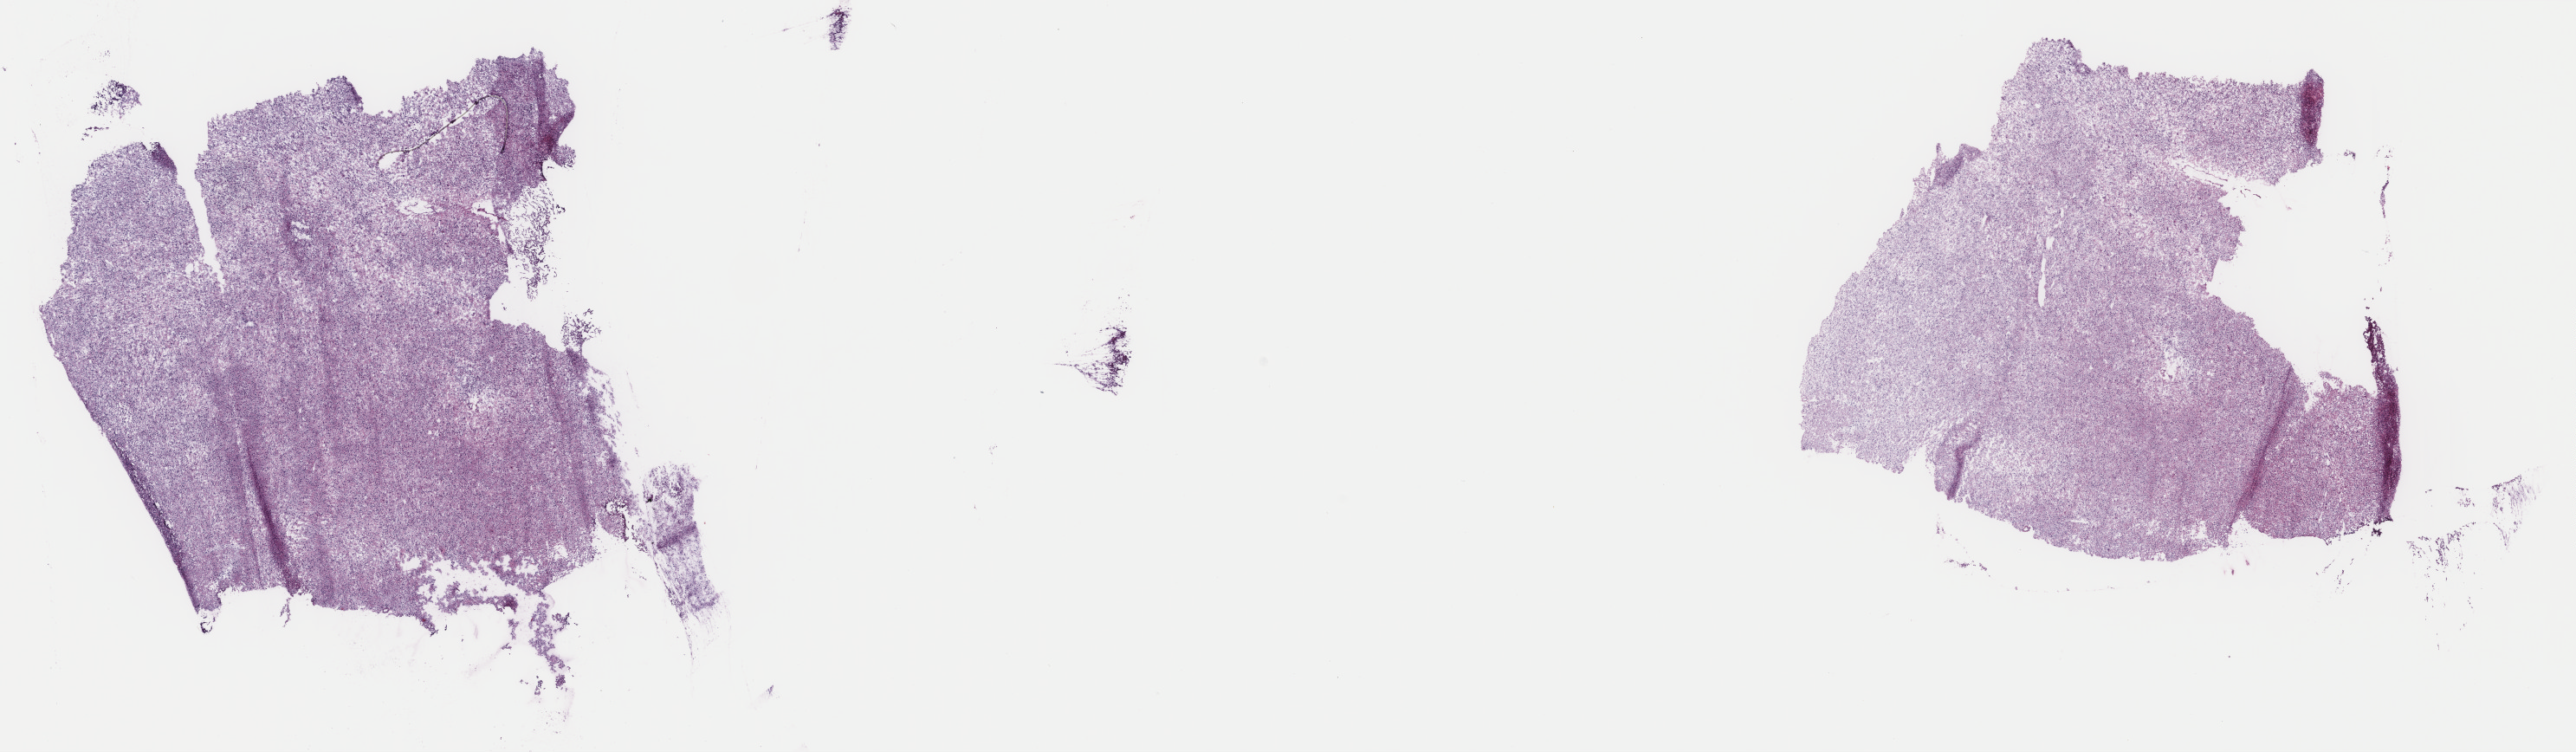
Digitized H&E-stained tissue section (whole slide) — low-resolution overview of the scanned area, about 23.6 x 6.9 mm, frozen section, primary tumour sample from the brain. Female, age 56 years at initial diagnosis. Histologic grade: G3 (poorly differentiated). Slide review estimates, as recorded: tumour cells 50%, tumour nuclei 90%, normal cells 10%, stromal cells 40%, necrosis 0%. Infiltration values recorded for this section: lymphocyte infiltration 0%, monocyte infiltration 0%, neutrophil infiltration 0%.
* diagnosis: Oligodendroglioma, anaplastic (cerebrum)
* laterality: left